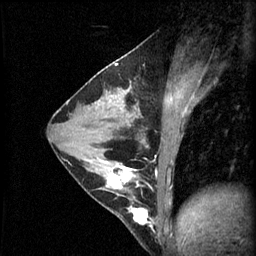
Breast MRI (dynamic contrast-enhanced), one sagittal slice. Slice 30 of 60 in the series (ordered by position). 3 images stored at this slice position (order not interpretable as contrast timing). 1.5 T. TE 4.2 ms, TR 11 ms. 2.1 mm slice thickness. 256 × 256 image matrix. Female patient, age 29 years.
Structures marked on this image (semi-automatically segmented with operator editing):
- analysis volume of interest (the breast-tissue region the enhancement analysis was run in; not a lesion): box from (x=93, y=164) to (x=153, y=229) px
- tumour enhancement mask (voxels above the 70 % enhancement threshold inside the analysis volume of interest): (x=104, y=166)–(x=152, y=227)